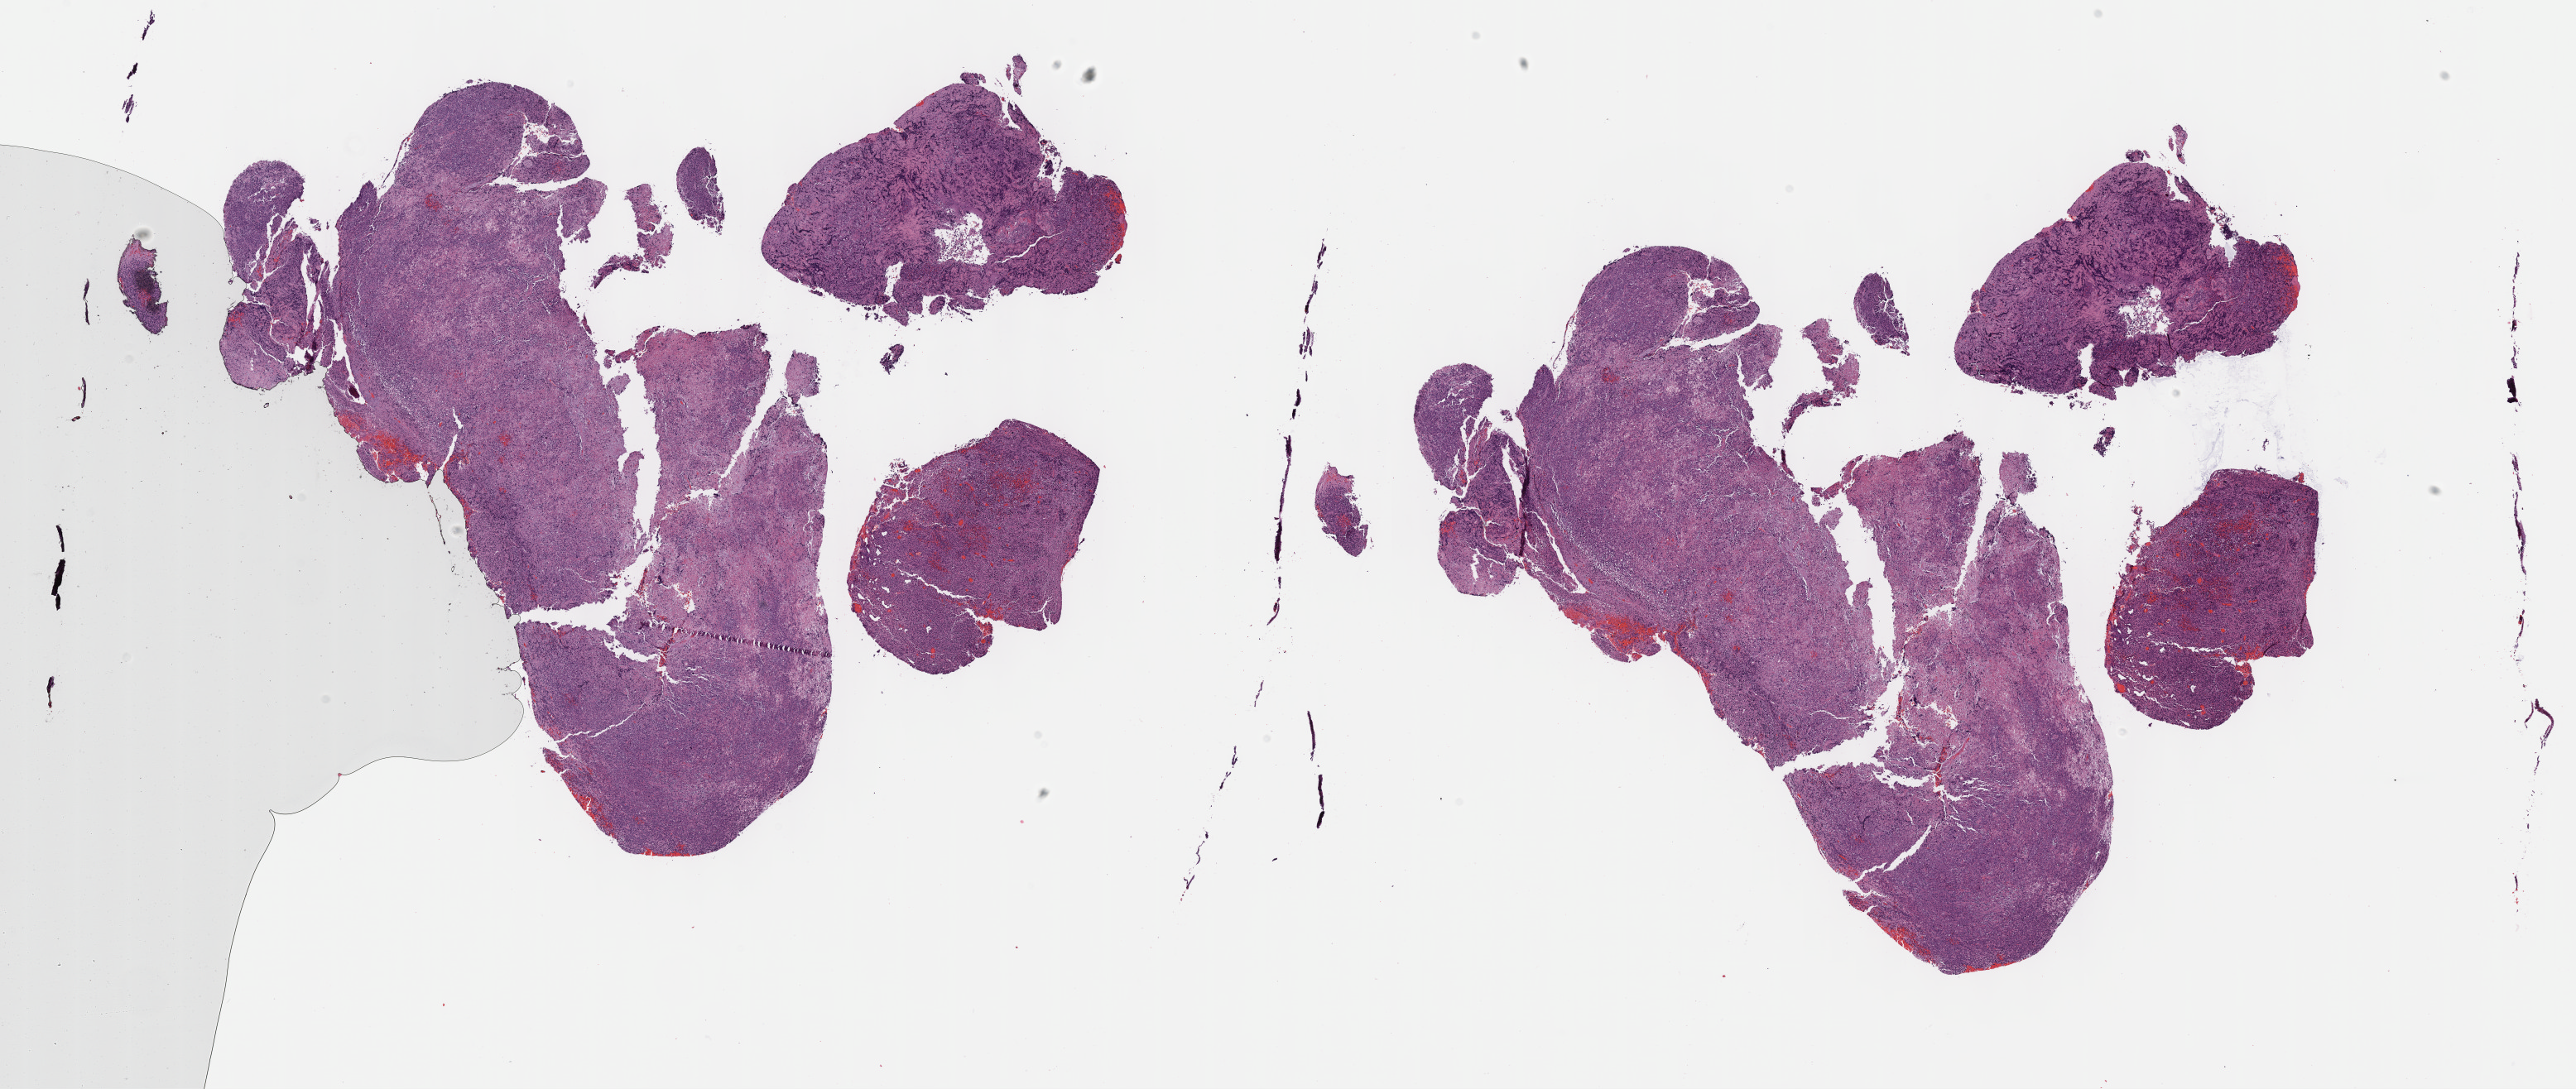
Whole-slide histology image, Hematoxylin and eosin (H&E) stained, a low-resolution overview of the entire scanned area, about 25.2 x 10.6 mm, FFPE section, lymphoid tissue, primary tumour sample. Female, age 63 years at initial diagnosis.
• pathologic diagnosis: Primary diffuse large B-cell lymphoma of the CNS (cerebellum, NOS)